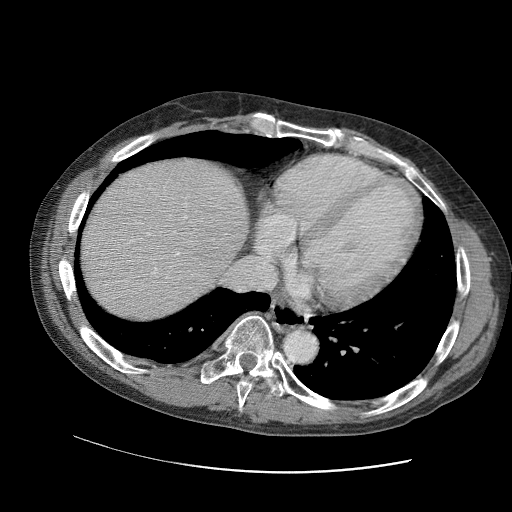
Contrast-enhanced abdominal CT (liver protocol), one axial slice. Slice 89 of 109 in the series (ordered by position). Reconstruction kernel STANDARD. 120 kVp. Soft-tissue window (W 400 / L 40 HU). 2.5 mm slice thickness. 512 × 512 image matrix. From the clinical record (not read from this slice): diagnosis: hepatocellular carcinoma (patient treated with transarterial chemoembolisation; whether this scan precedes or follows treatment is not stated here); TNM stage (as recorded): Stage-IIIC; Child-Pugh class: B; tumour differentiation: well differentiated; tumour nodularity: uninodular.
Annotated regions visible in this slice (semi-automatic segmentation, software-assisted and operator-edited):
- liver parenchyma outside the tumour (the mass and vessels are separate outlines, so this box may not span the whole liver): bounding box (x1, y1, x2, y2) in pixels: (80, 156, 246, 320)
- liver vessels: (128, 184, 219, 281)